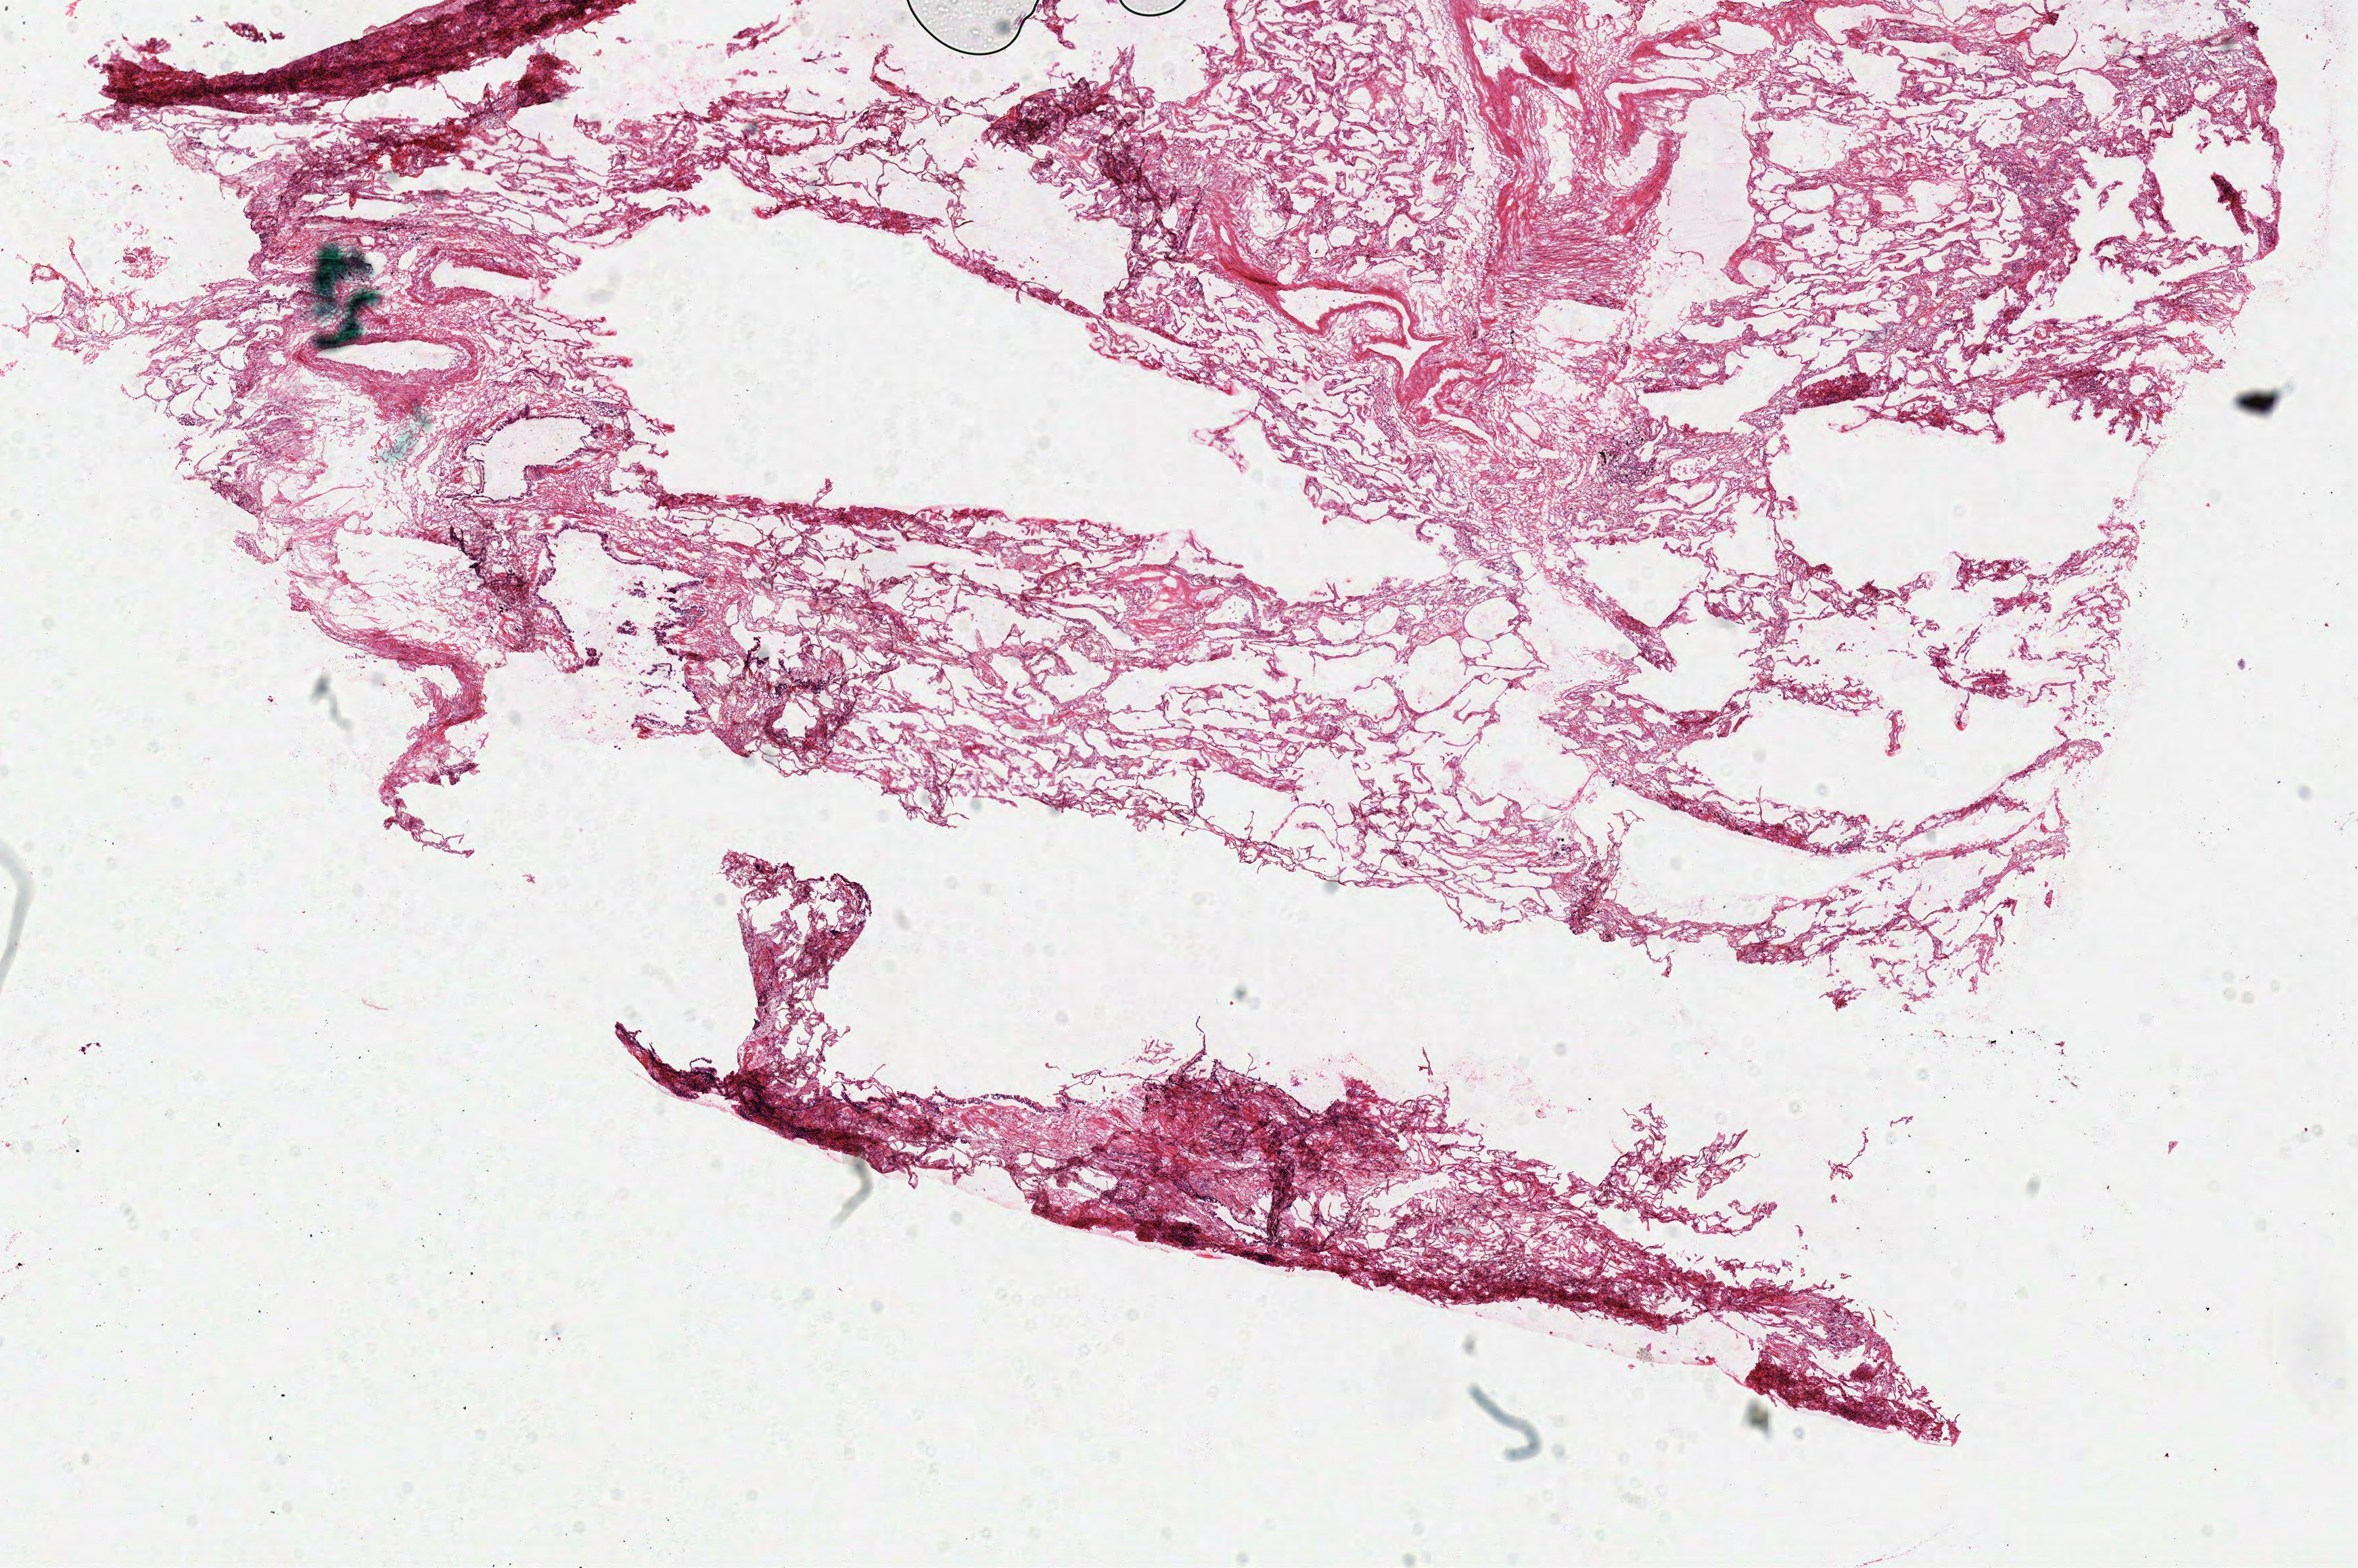
Hematoxylin and eosin (H&E) stained whole-slide image, whole scanned area (about 13.7 x 9.1 mm, slide scanned at 40x) shown as a low-resolution overview; frozen section from the top of the tissue portion; sample: solid tissue normal (non-tumour tissue), lung. Female, age 86 years at initial diagnosis.
- this section: solid tissue normal (non-tumour) sample from the same patient
- patient diagnosis: Adenocarcinoma, NOS